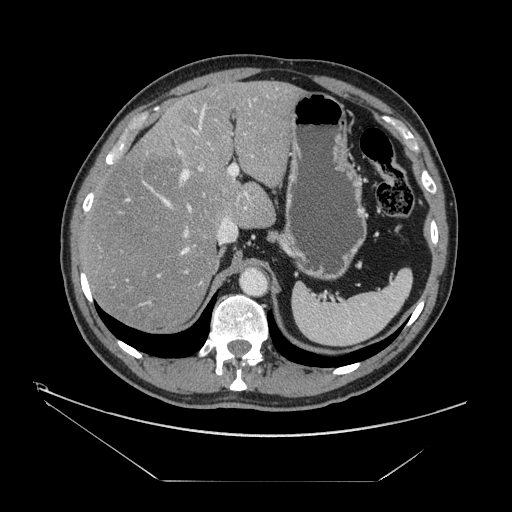
Contrast-enhanced abdominal CT, one axial slice. Position 104 of 161 along the scan axis. Reconstruction kernel STANDARD. 120 kVp. Soft-tissue window (W 400 / L 40 HU). 2.5 mm slice thickness. 512 × 512 image matrix, field of view 440 × 440 mm. Male patient, age 65 years. Case-level facts recorded for this patient, not image findings: diagnosis: colorectal cancer liver metastases, imaged before liver resection.
Structures marked on this image (outlined manually by an expert reader):
- hepatic veins: box from (x=127, y=111) to (x=203, y=281) px
- liver: (x=83, y=82)–(x=299, y=329)
- planned liver remnant (the part of the liver to remain after resection): (x=82, y=82)–(x=299, y=329)
- portal vein (with intrahepatic branches): (x=111, y=88)–(x=278, y=306)
- liver metastasis: (x=173, y=143)–(x=177, y=147)